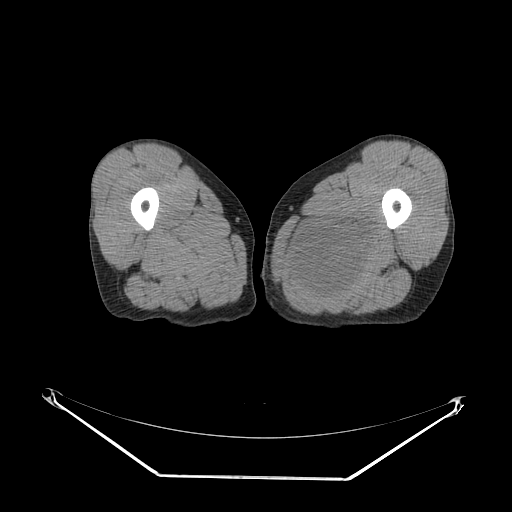
CT of an extremity soft-tissue mass (from a PET/CT study), one axial slice. Slice 20 of 267 in the series (ordered by position). Soft-tissue window (W 400 / L 40 HU). 3.75 mm slice thickness. 512 × 512 image matrix, field of view 500 × 500 mm. Male patient. From the clinical record (not read from this slice): histological type: pleiomorphic liposarcoma; grade: high; site of the primary tumour: left thigh.
Structures marked on this image (expert contour drawn on MRI and transferred to this co-registered scan by the dataset authors):
- gross tumour volume including surrounding oedema: bounding box <292,210,382,302> (left, top, right, bottom; pixels)
- gross tumour volume (mass): <297,221,368,296>